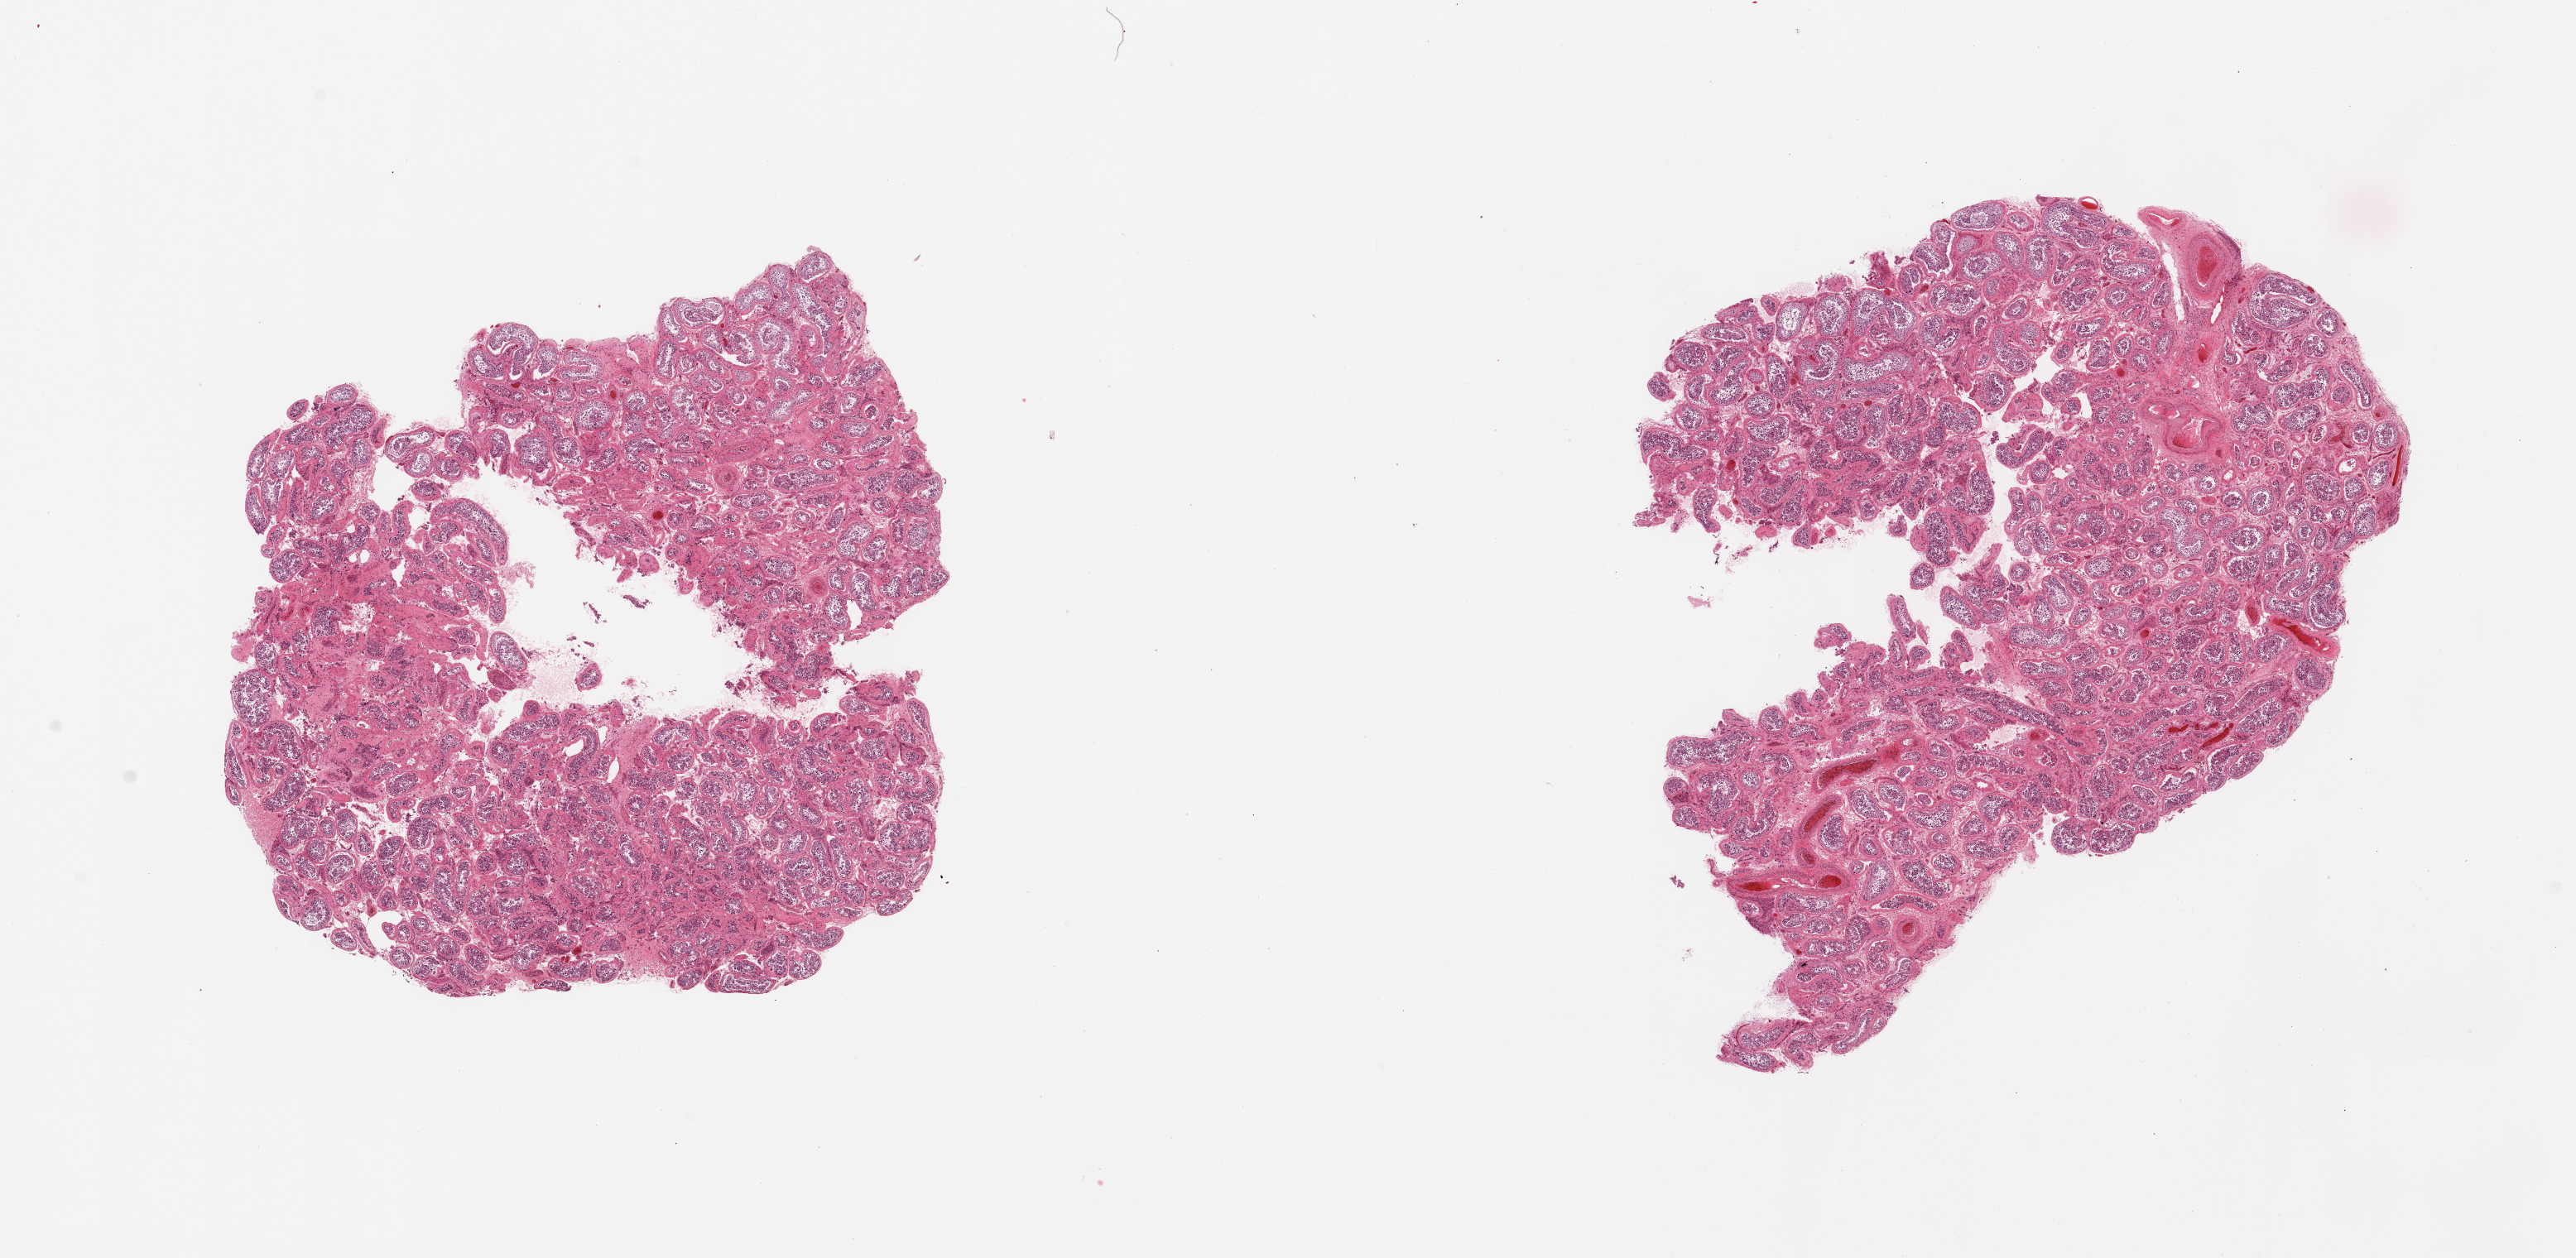
Haematoxylin and eosin whole-slide image — low-resolution overview of the scanned area, about 24.6 x 12.0 mm, PAXgene-fixed, paraffin-embedded tissue, target tissue: testis, tissue donor sample.
Pathologist's review note for this sample: 2 pieces, spermatogenesis appears reduced.